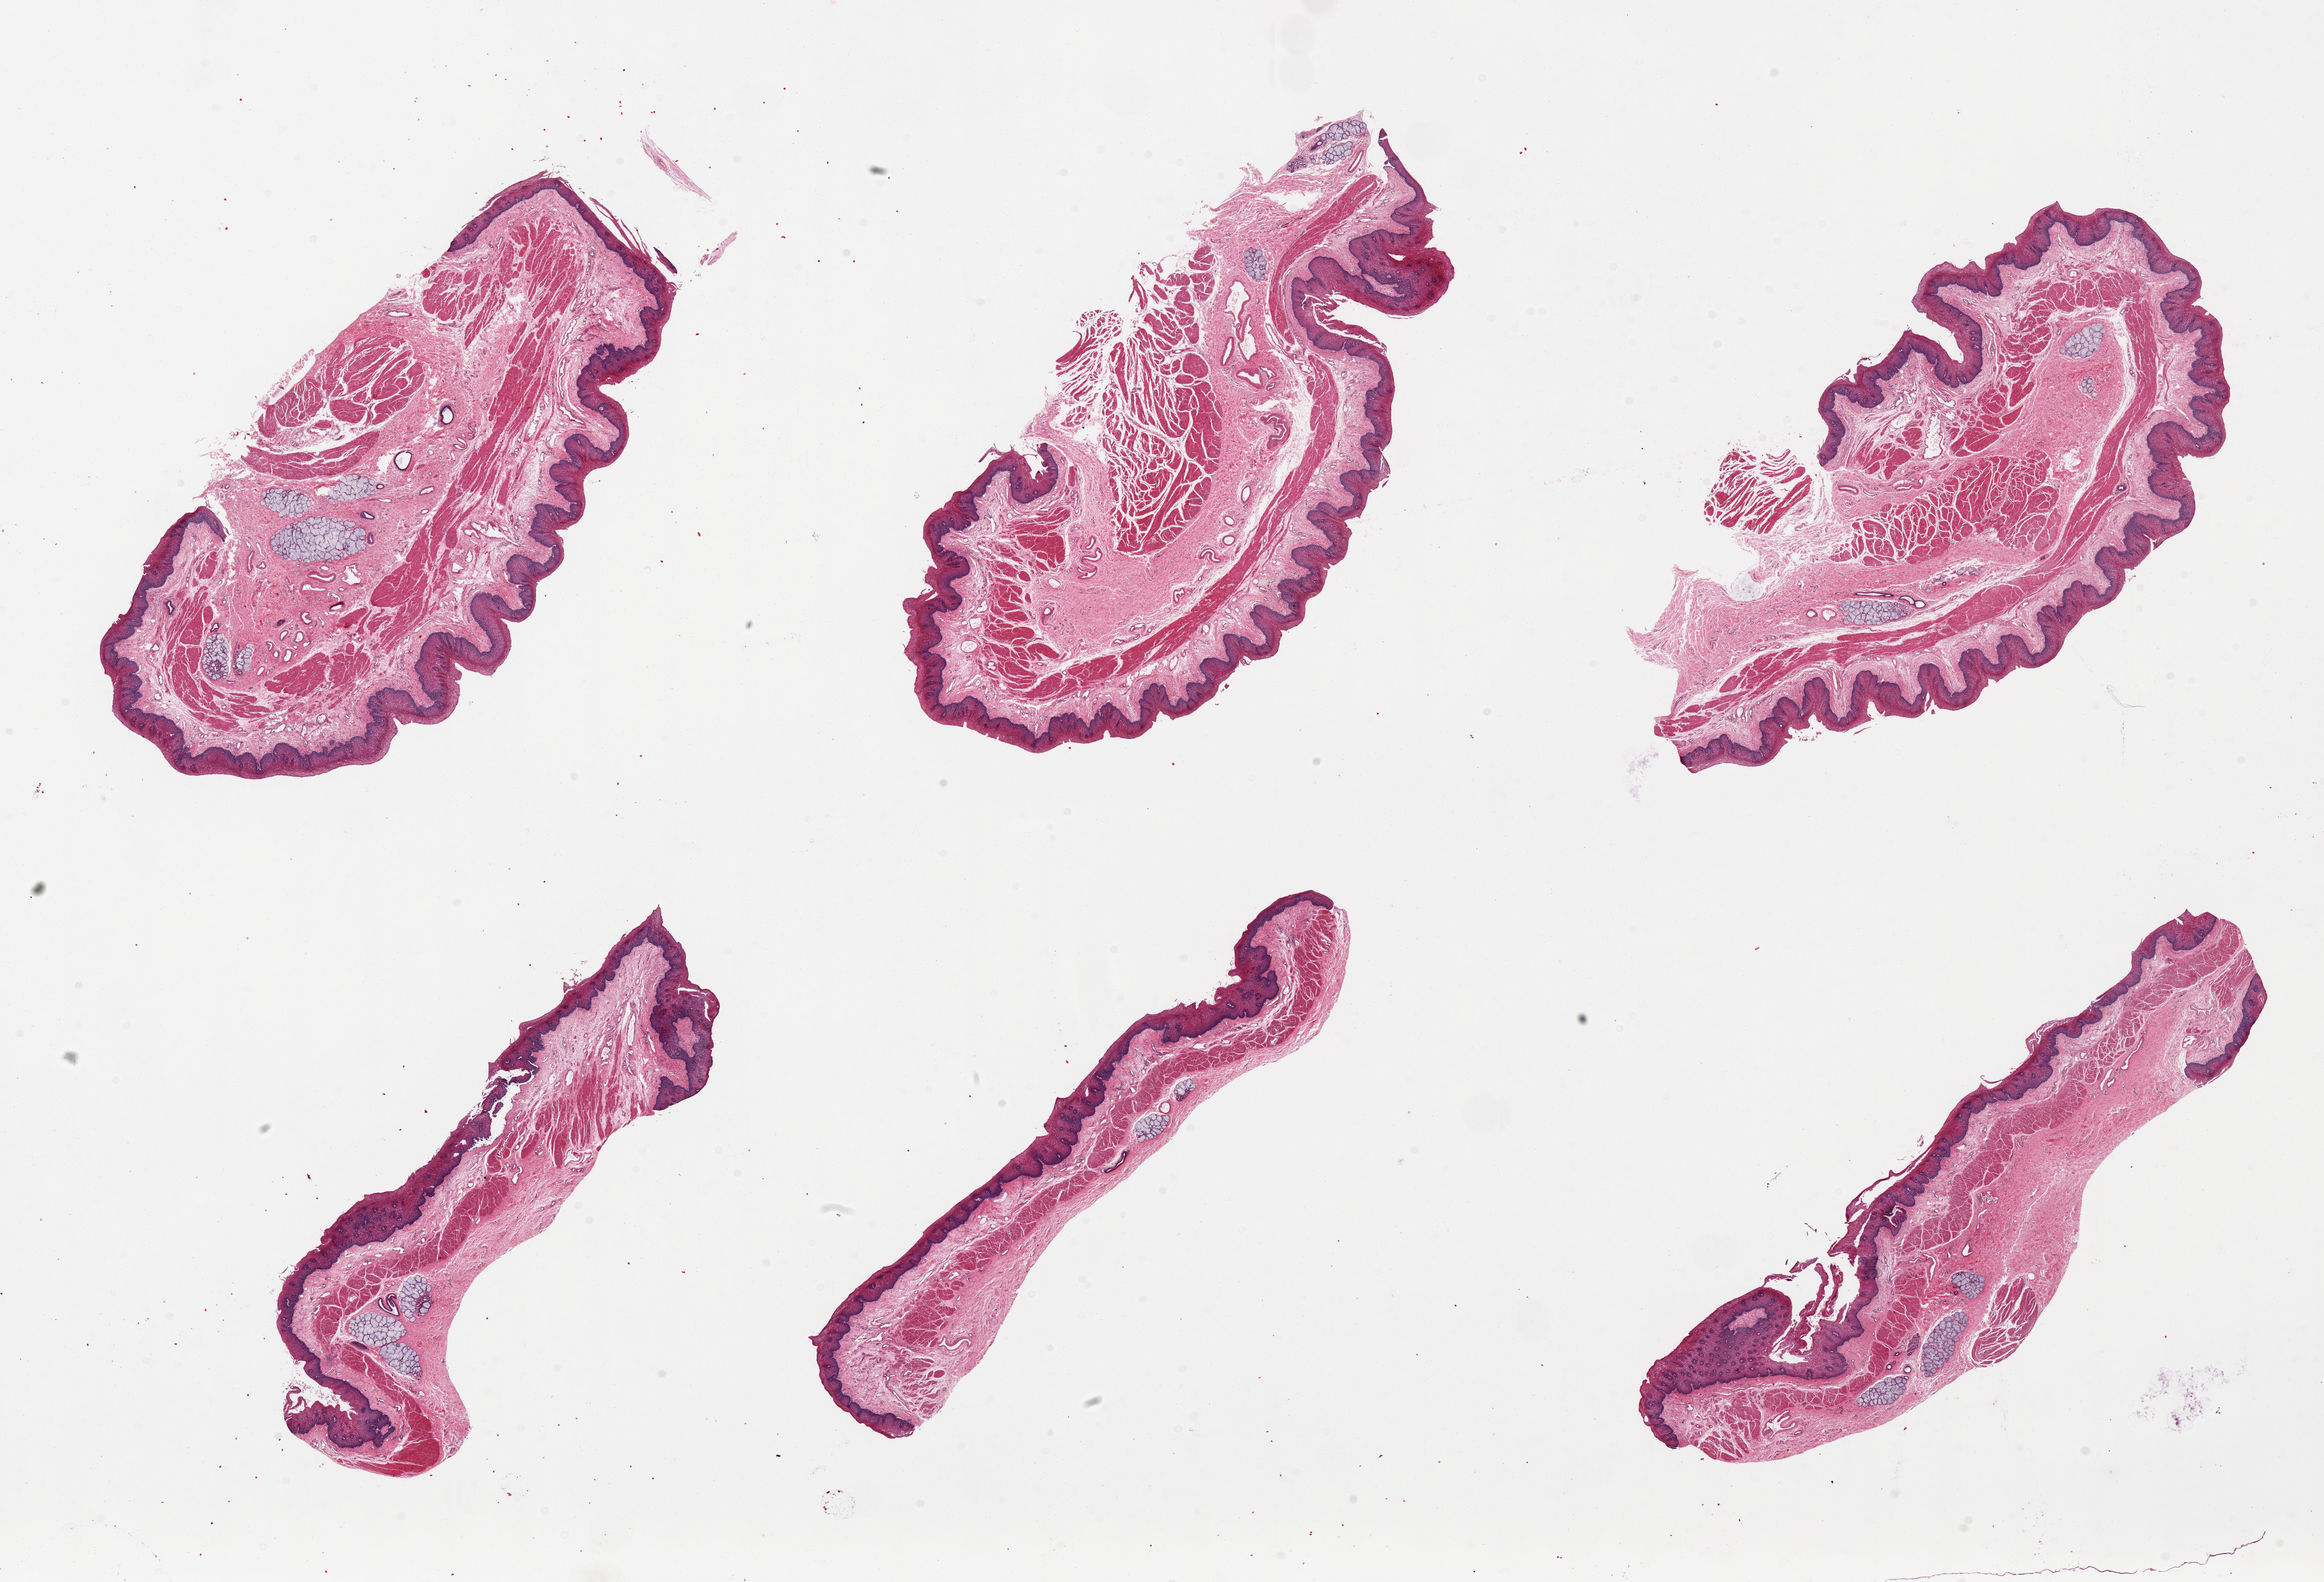
Whole-slide image, H&E stain — low-resolution overview of the scanned area, about 30.5 x 20.8 mm. PAXgene-fixed paraffin-embedded (PFPE) section. Target tissue: esophageal mucous membrane. Donor tissue sample. Female donor.
Review note (as recorded): 6 pieces; up to 10x5mm; Well preserved mucosa; 2 have muscularis propria up to 2 x 3 mm.